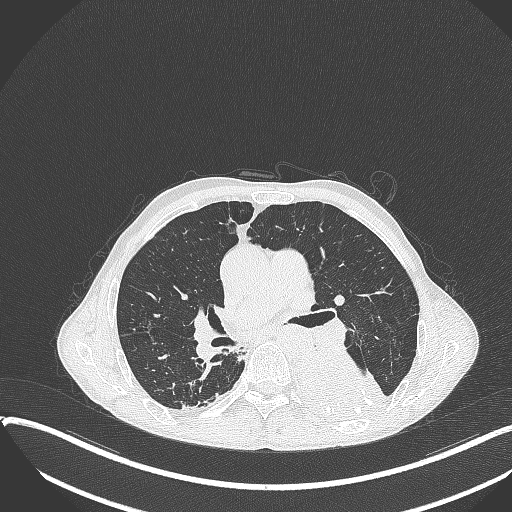
Chest CT, one axial slice. Position 217 of 401 along the scan axis. Reconstruction kernel B70f. Lung window (W 1500 / L -600 HU). 1 mm slice thickness. 512 × 512 image matrix, field of view 400 × 400 mm. Patient: male, 57 years. From the clinical record (not read from this slice): clinical TNM (as recorded): T4 N0 M0.
Structures marked on this image (bounding box drawn by a radiologist):
- lung tumour (recorded histology: squamous cell carcinoma): box from (x=293, y=349) to (x=392, y=424) px